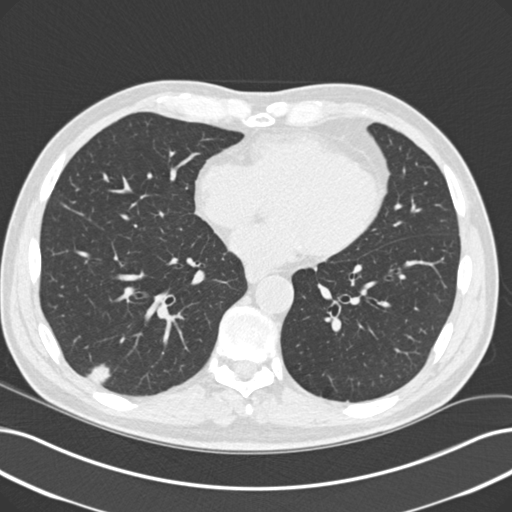
Axial slice from a low-dose chest CT screening exam; baseline annual screen; lung window (W 1500 / L -600 HU); 2 mm slice thickness; standard (soft-tissue) reconstruction kernel (B30f); slice 137 of 229 in the series. Male, age 60 years at enrolment.
Expert reader's lesion annotation, bounding box (x1, y1, x2, y2) in pixels: (75, 357, 118, 402). The screening reader recorded 2 non-calcified nodules or masses ≥4 mm on this exam; which of them this box marks is not recorded. Official screen result: positive, change unspecified: nodule(s) >= 4 mm or enlarging nodule(s), mass(es), or other non-specific abnormalities suspicious for lung cancer. Participant outcome: lung cancer diagnosed 64 days after this screen — acinar cell carcinoma, right lower lobe, moderately differentiated (G2), stage IA (AJCC 6th edition), 16 mm at pathology.